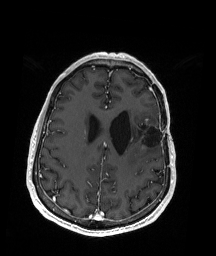
Brain MRI from a brain-tumour surgery series, one axial slice. Position 67 of 192 along the scan axis. T1-weighted post-contrast. 1 mm slice thickness. 216 × 256 image matrix, field of view 211 × 250 mm. Case-level facts recorded for this patient, not image findings: histopathology: Oligodendroglioma; WHO grade: 2; IDH mutation: yes.
Annotated regions visible in this slice (manually delineated by an expert):
- previous resection cavity: bounding box (x1, y1, x2, y2) in pixels: (132, 122, 163, 146)
- tumour: (142, 119, 149, 150)